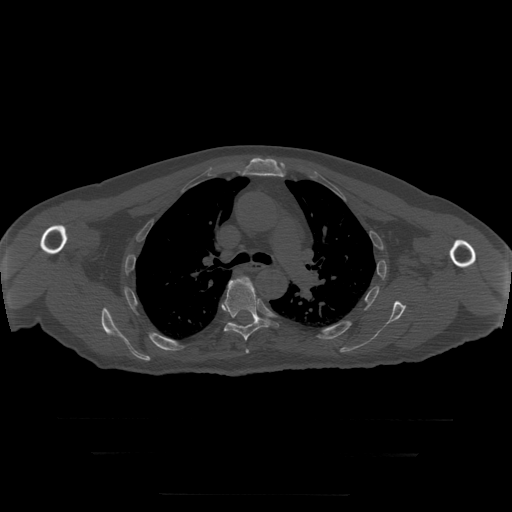
CT including the spine, one axial slice; position 209 of 397 along the scan axis; 120 kVp; bone window (W 1800 / L 400 HU); 512 × 512 image matrix, field of view 510 × 510 mm. Patient age 73 years. From the clinical record (not read from this slice): primary cancer: prostate.
Outlined on this slice (semi-automatically segmented with operator editing):
- T5 vertebra: bounding box [x1, y1, x2, y2] px = [246, 349, 249, 354]
- T6 vertebra: [224, 277, 271, 341]